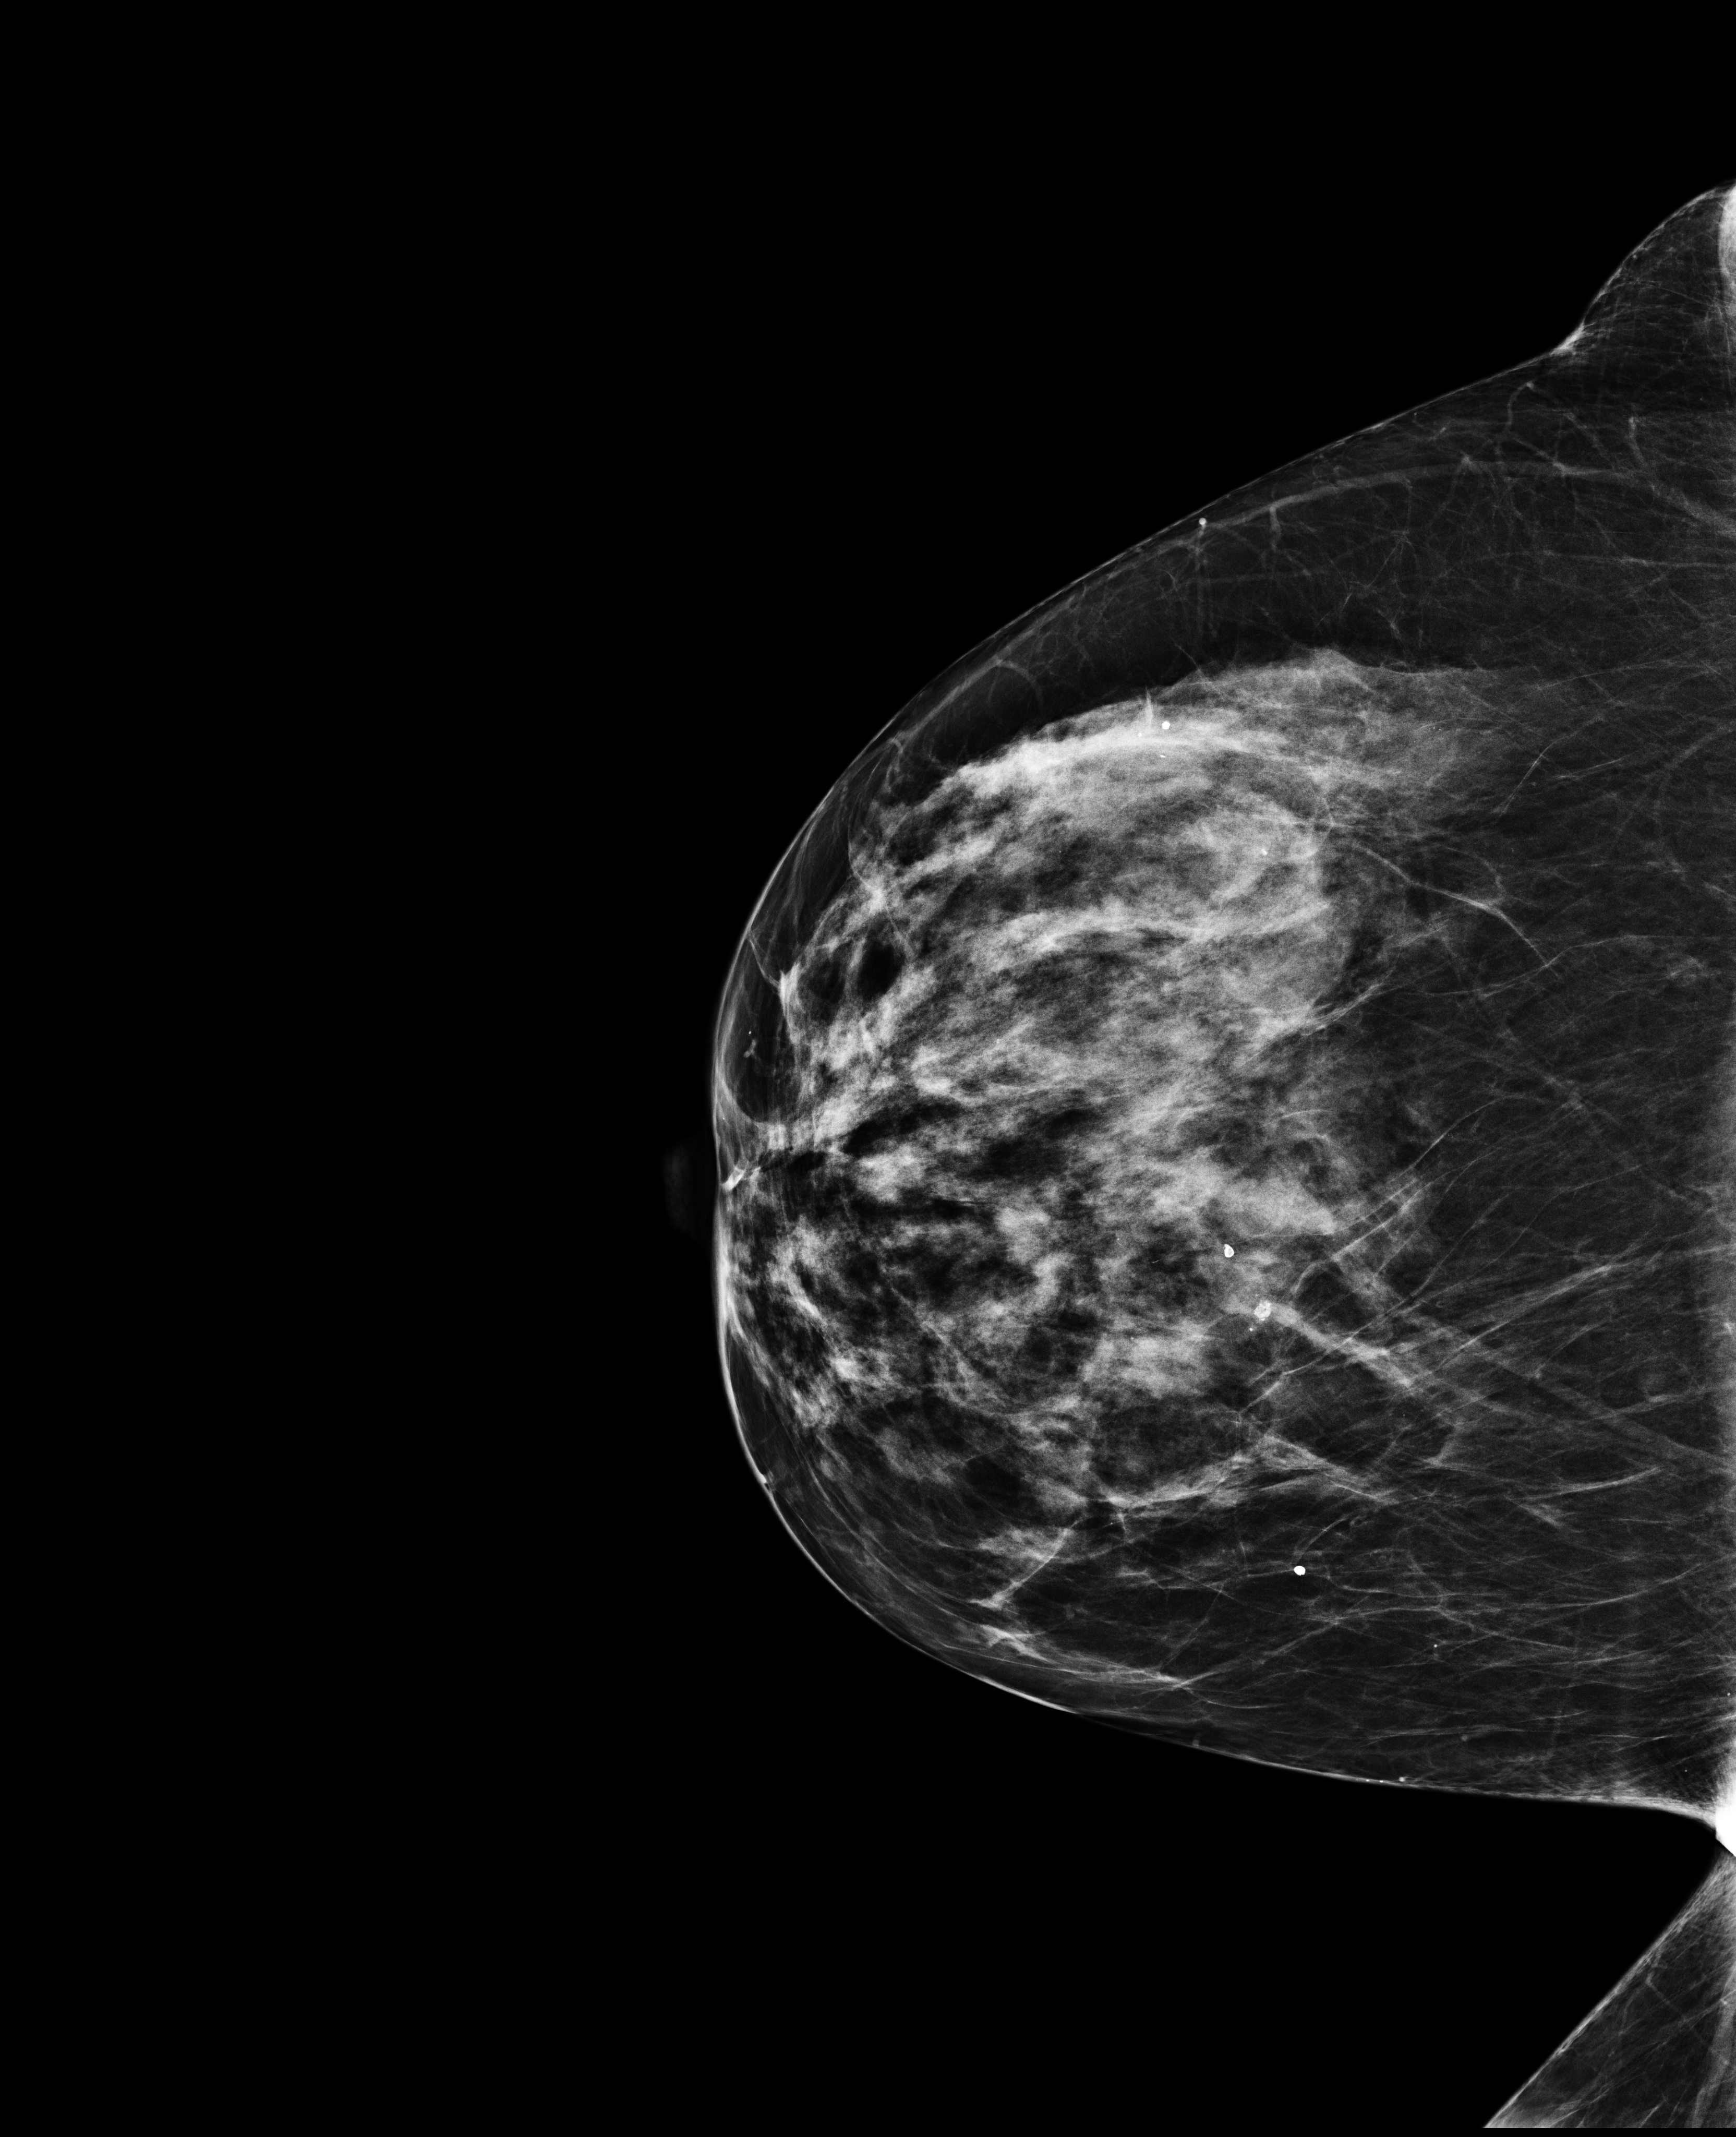
Full-field digital mammogram (FFDM); right breast; CC view; annual screening mammography examination. Patient: female, 62 years.
BI-RADS breast density category at the screening exam (both breasts, scale 1–4): 3. Final BI-RADS category for the screening round (tomosynthesis exam, both breasts): category 2. Recall: no recall after this screen.